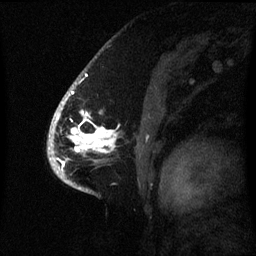
Breast MRI (dynamic contrast-enhanced), one sagittal slice. Dynamic contrast-enhanced series, image 2 of 3 at this slice position (ordered by acquisition). 1.5 T. TE 4.2 ms, TR 8.4 ms. 2.1 mm slice thickness. 256 × 256 image matrix, field of view 220 × 220 mm. Patient: female, 53 years. From the clinical record (not read from this slice): setting: breast cancer imaged before/during neoadjuvant chemotherapy; receptor status: HR-positive, HER2-negative.
Annotated regions visible in this slice (semi-automatic segmentation, software-assisted and operator-edited):
- analysis volume of interest (the breast-tissue region the enhancement analysis was run in; not a lesion): box from (x=52, y=90) to (x=121, y=171) px
- tumour enhancement mask (voxels above the 70 % enhancement threshold inside the analysis volume of interest): (x=55, y=94)–(x=115, y=171)